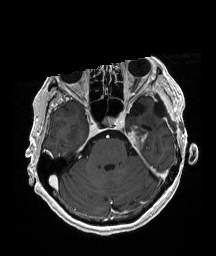
Brain MRI from a brain-tumour surgery series, one axial slice. Position 133 of 192 along the scan axis. T1-weighted post-contrast. 216 × 256 image matrix. From the clinical record (not read from this slice): histopathology: Glioblastoma; WHO grade: 4; IDH mutation: no; tumour location: Left Temporal.
Annotated regions visible in this slice (outlined manually by an expert reader):
- previous resection cavity: bounding box (x1, y1, x2, y2) in pixels: (154, 104, 162, 114)